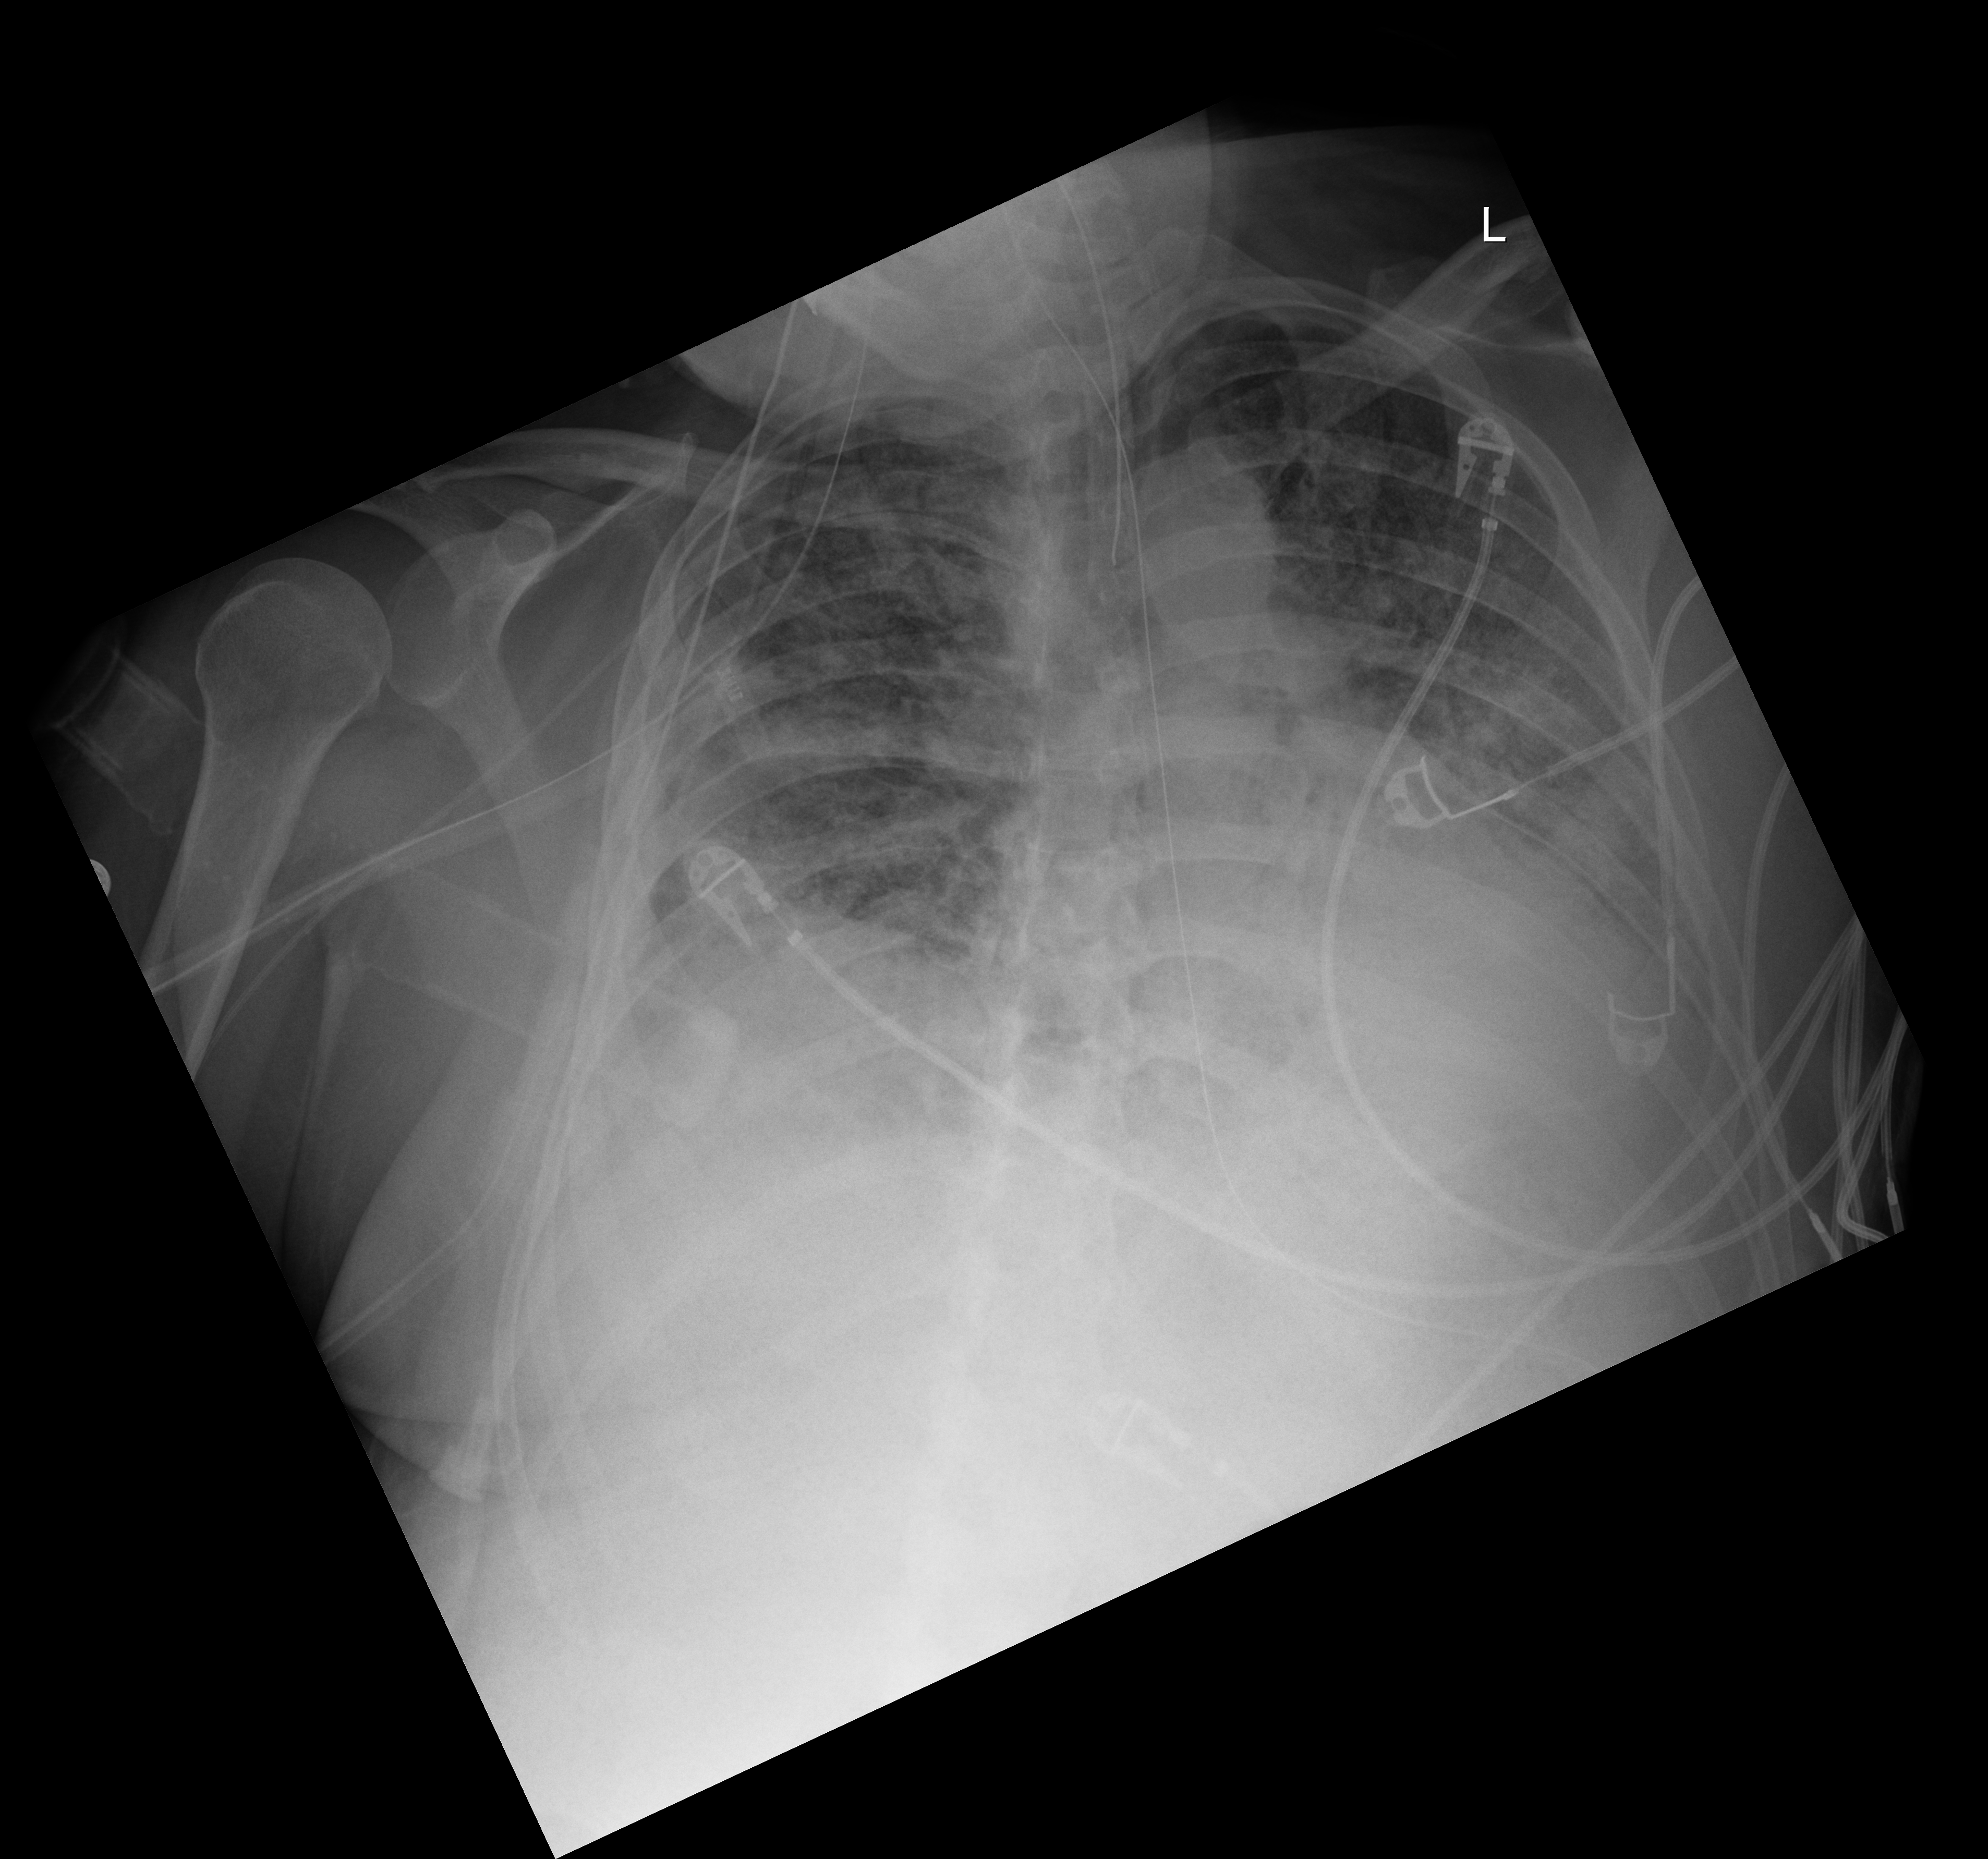
Bedside chest radiograph (digital radiography). Male patient hospitalised with COVID-19, age 18–59 years.
From the hospital-stay record, not from the radiograph (when in the stay this image was taken is not recorded): admitted to intensive care during this hospital stay: yes; mechanically ventilated during this hospital stay: yes.